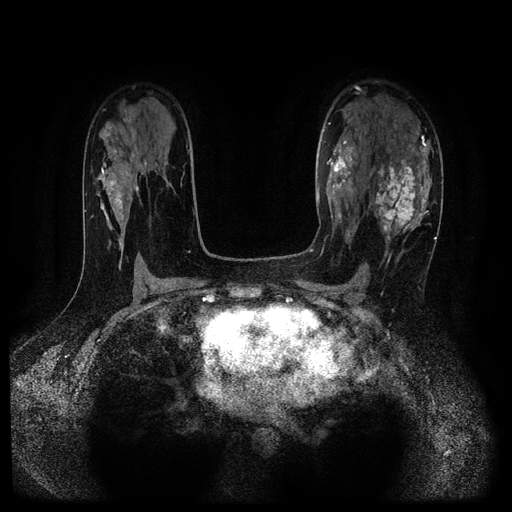
Breast MRI (dynamic contrast-enhanced, multi-phase), one axial slice; slice 67 of 116 in the series (ordered by position); dynamic contrast-enhanced series, time point 2 of 5 at this slice position (early post-contrast); 1.5 T; TE 2.7 ms, TR 5.4 ms; 2.2 mm slice thickness; 512 × 512 image matrix, field of view 330 × 330 mm. Patient: female, 43 years.
Annotated regions visible in this slice (semi-automatic segmentation, software-assisted and operator-edited):
- breast lesion (labelled 'tumour' in the annotation; benign lesions carry a separate 'benign' label): bounding box <370,158,421,265> (left, top, right, bottom; pixels)
- breast lesion (labelled benign in the annotation): <326,140,356,198>